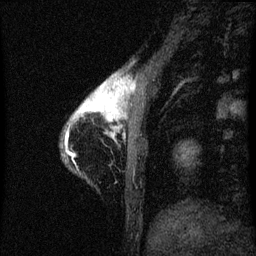
Breast MRI (dynamic contrast-enhanced), one sagittal slice. Position 8 of 60 along the scan axis. Dynamic contrast-enhanced series, image 2 of 3 at this slice position (ordered by acquisition). 1.5 T. TE 4.2 ms, TR 8 ms. 256 × 256 image matrix. Patient: female, 38 years.
Structures marked on this image (semi-automatically segmented with operator editing):
- analysis volume of interest (the breast-tissue region the enhancement analysis was run in; not a lesion): box from (x=64, y=76) to (x=128, y=147) px
- tumour enhancement mask (voxels above the 70 % enhancement threshold inside the analysis volume of interest): (x=66, y=78)–(x=128, y=135)